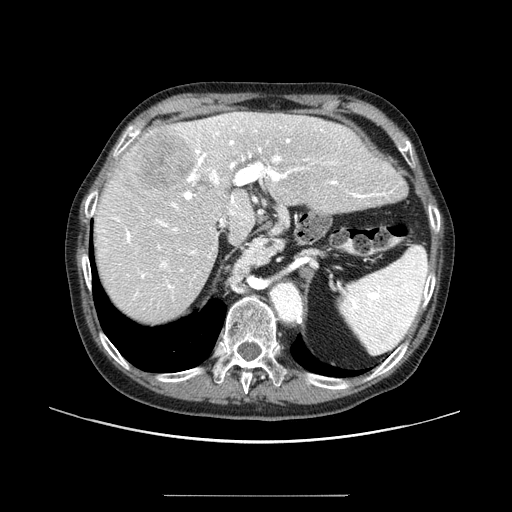
Contrast-enhanced abdominal CT (liver protocol), one axial slice. Position 64 of 91 along the scan axis. One of 2 acquisitions stored at this slice position. Soft-tissue window (W 400 / L 40 HU). 2.5 mm slice thickness. 512 × 512 image matrix, field of view 400 × 400 mm. From the clinical record (not read from this slice): diagnosis: hepatocellular carcinoma (patient treated with transarterial chemoembolisation; whether this scan precedes or follows treatment is not stated here); TNM stage (as recorded): Stage-I; Child-Pugh class: A; tumour differentiation: moderately differentiated; tumour nodularity: uninodular.
Annotated regions visible in this slice (semi-automatically segmented with operator editing):
- liver parenchyma outside the tumour (the mass and vessels are separate outlines, so this box may not span the whole liver): bounding box <94,112,400,322> (left, top, right, bottom; pixels)
- mass: <122,128,194,192>
- liver vessels: <101,113,393,297>